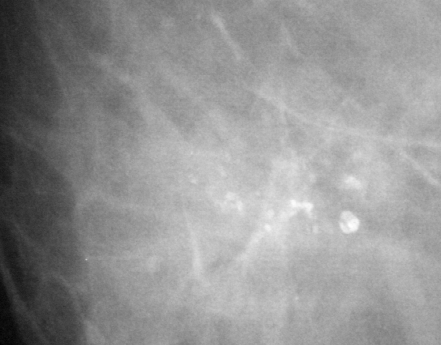
Region of interest cut from a scanned film mammogram (one marked finding), right breast, CC view.
Finding: calcifications, morphology pleomorphic, distribution clustered; BI-RADS assessment category 4; pathology result (as recorded, not read from the image): benign.